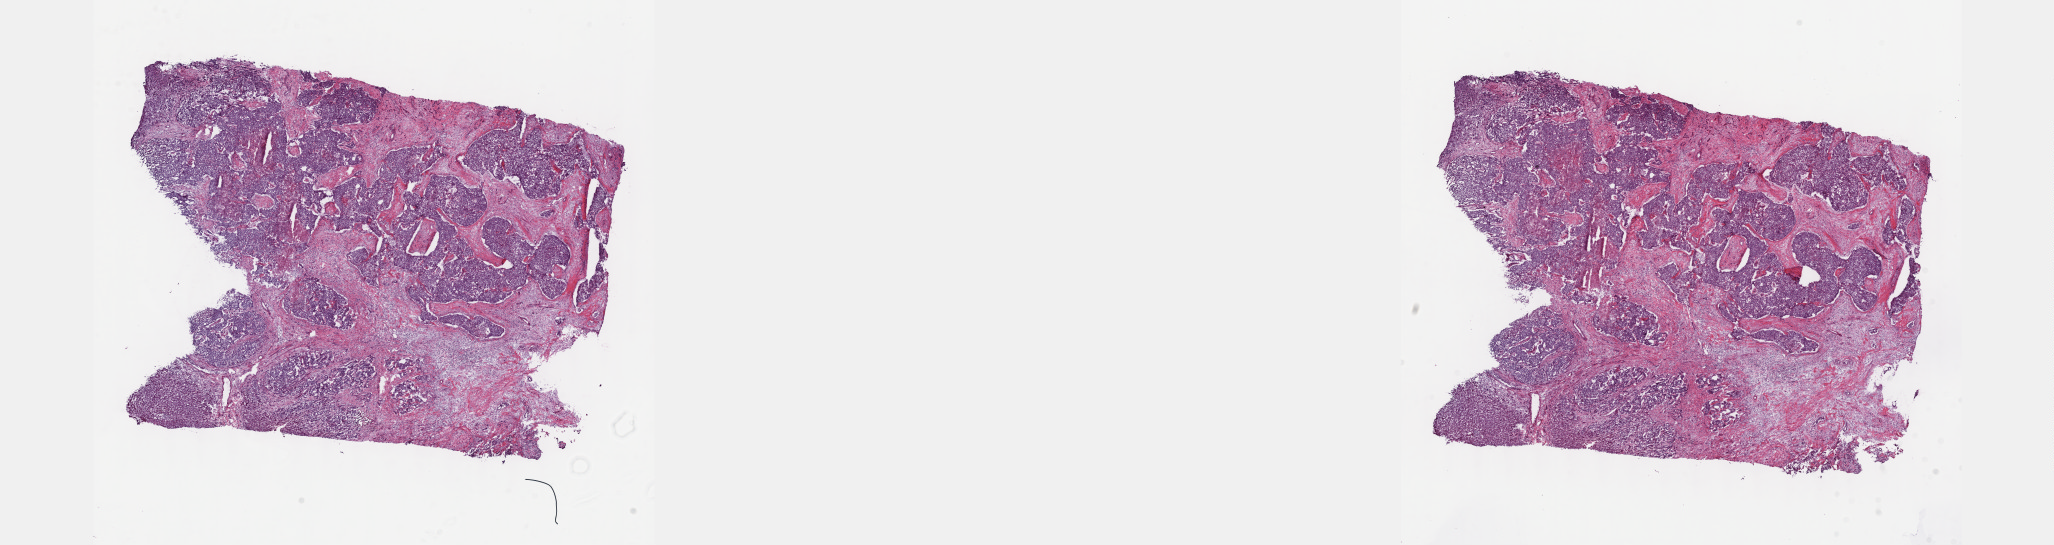
H&E-stained whole-slide image — low-resolution overview of the scanned area, about 33.2 x 8.8 mm (slide scanned at 40x), frozen section from the top of the tissue portion, primary tumour sample from the bile duct. Patient: male, age at initial diagnosis 71 years. Histologic grade: G3 (poorly differentiated). Slide review estimates, as recorded: tumour cells 95%, tumour nuclei 60%, normal cells 0%, stromal cells 0%, necrosis 5%. Infiltration values recorded for this section: lymphocyte infiltration 10%, monocyte infiltration 0%, neutrophil infiltration 0%.
Histologic diagnosis: Cholangiocarcinoma (intrahepatic bile duct). AJCC pathologic stage: I (7th edition).